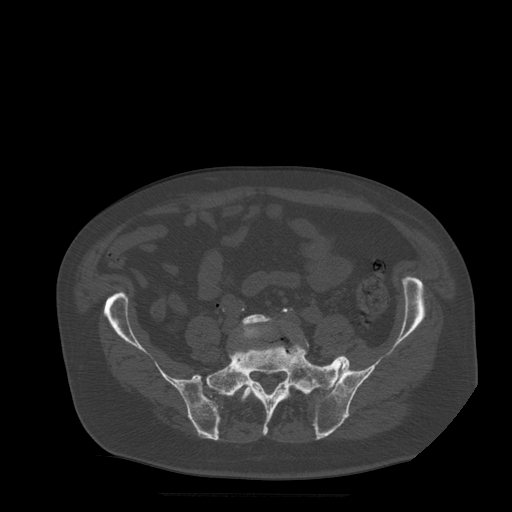
CT including the spine, one axial slice. Slice 71 of 522 in the series (ordered by position). Bone window (W 1800 / L 400 HU). 512 × 512 image matrix, field of view 420 × 420 mm. Patient age 72 years. Case-level facts recorded for this patient, not image findings: primary cancer: prostate.
Structures marked on this image (semi-automatic segmentation, software-assisted and operator-edited):
- L5 vertebra: bounding box [x1, y1, x2, y2] px = [239, 315, 310, 399]